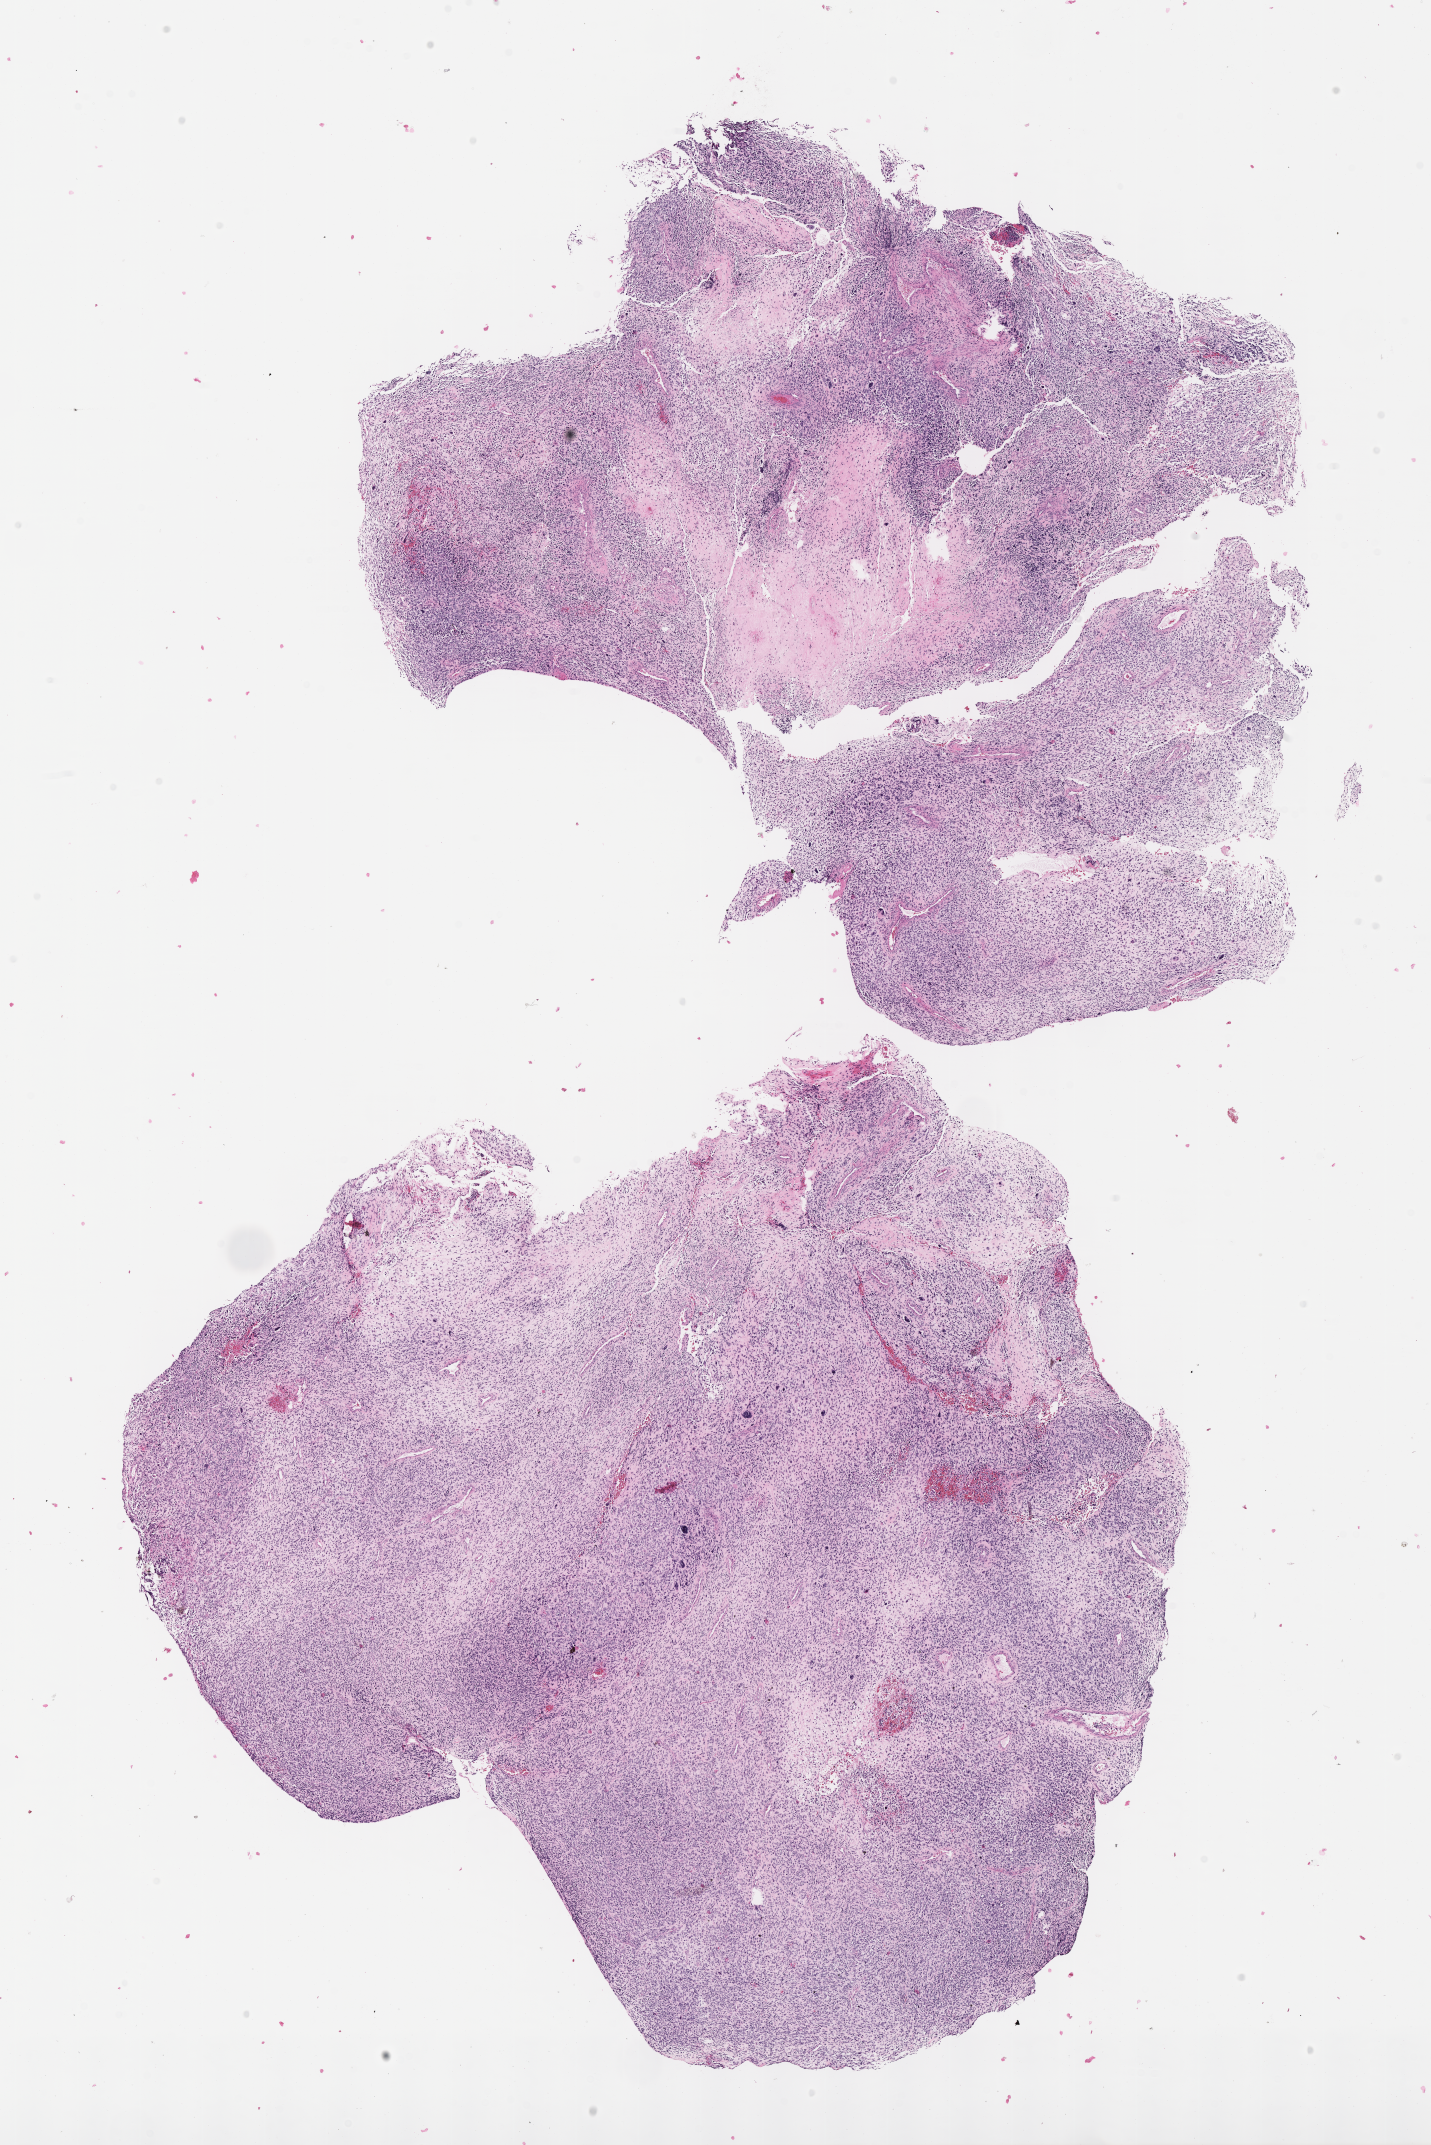
Digitized haematoxylin and eosin-stained section of tumor tissue — low-resolution overview of the scanned area, about 11.6 x 17.3 mm, formalin-fixed, paraffin-embedded (FFPE) tissue, site: nasopharynx. Patient: male, age 5.5 years at diagnosis.
Metastatic status at presentation (as recorded): non-metastatic (confirmed). Stage (as recorded): 2. Diagnosis: rhabdomyosarcoma; histological classification: embryonal rhabdomyosarcoma.